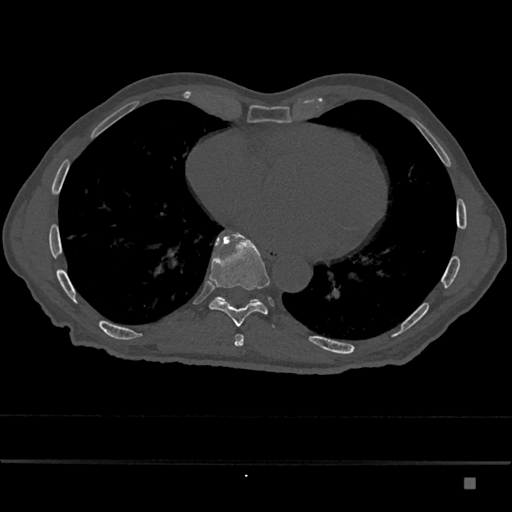
CT including the spine, one axial slice; 120 kVp; bone window (W 1800 / L 400 HU); 0.5 mm slice thickness; 512 × 512 image matrix, field of view 390 × 390 mm. Male patient, age 72 years. Case-level facts recorded for this patient, not image findings: primary cancer: prostate.
Outlined on this slice (semi-automatically segmented with operator editing):
- T10 vertebra: box from (x=215, y=296) to (x=260, y=303) px
- T9 vertebra: (x=209, y=230)–(x=270, y=327)